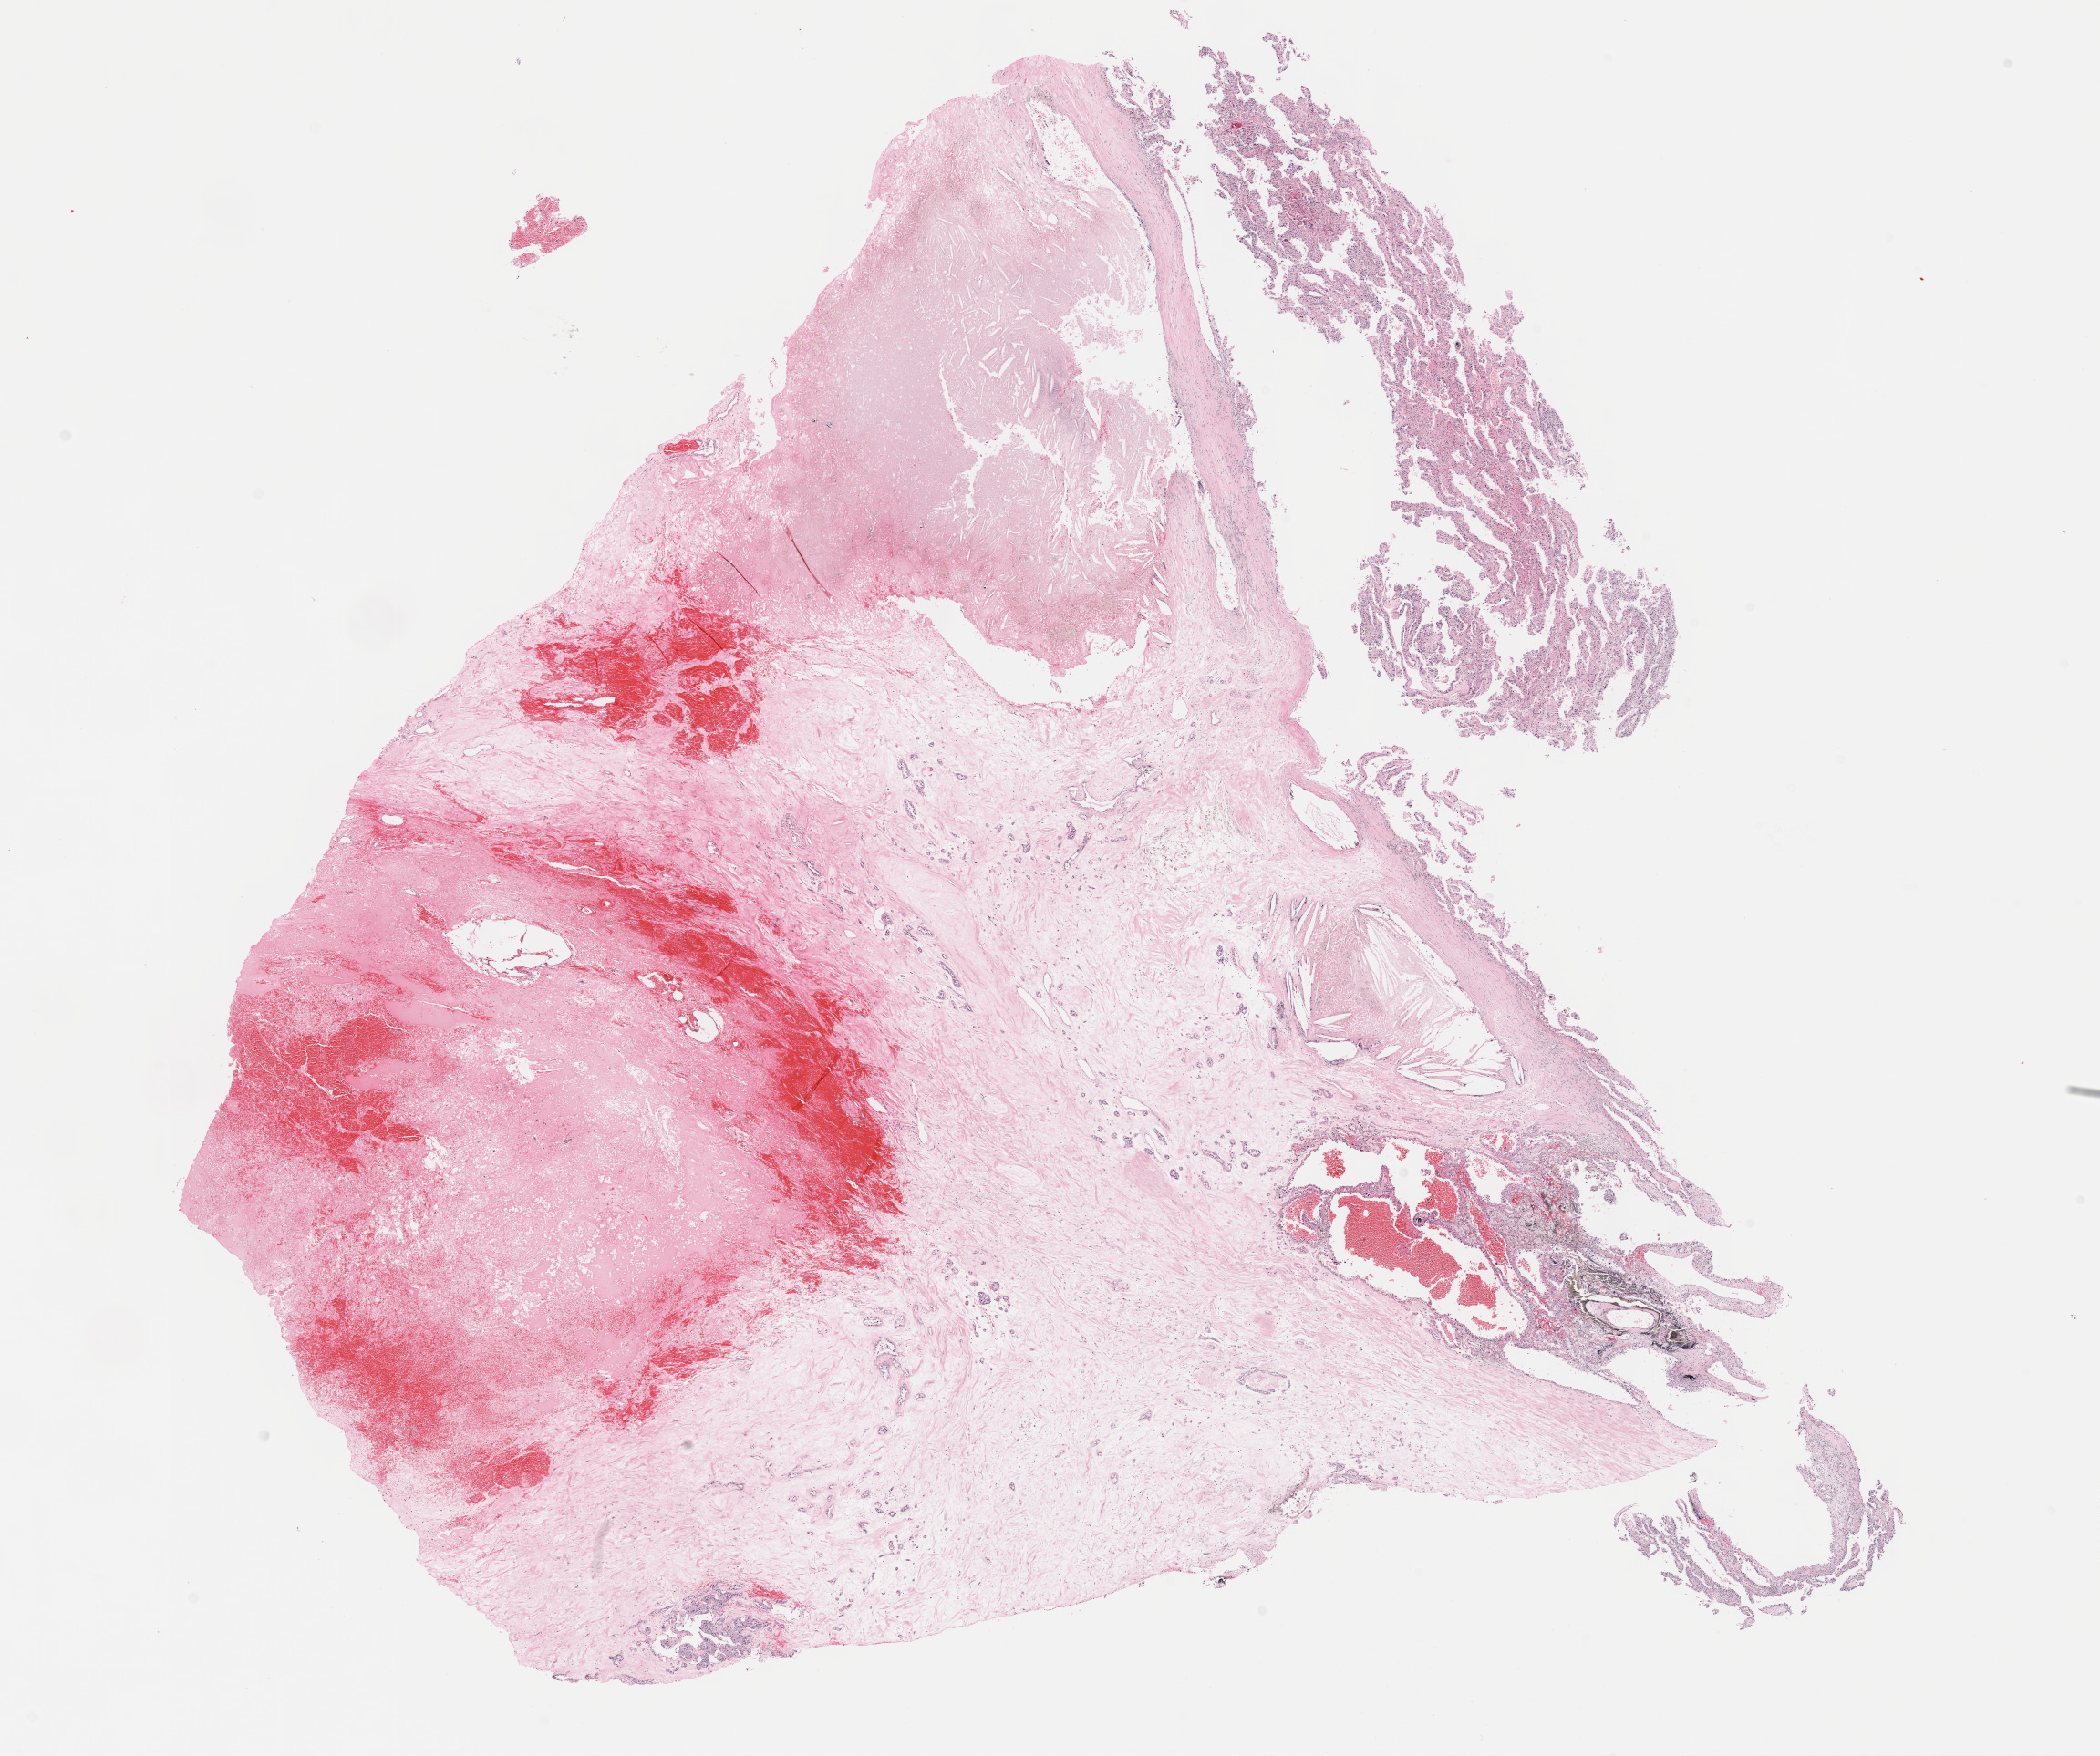
Whole-slide histology image, Hematoxylin and eosin (H&E) stained — low-resolution overview of the scanned area, about 18.6 x 15.6 mm (slide scanned at 40x); formalin-fixed paraffin-embedded (FFPE) diagnostic section; sample: primary tumour, kidney. Male patient; age at initial diagnosis 48 years. Histologic grade: G3 (poorly differentiated).
TNM: T2 N0 M0. Diagnosis: Clear cell adenocarcinoma, NOS. AJCC pathologic stage: II. Laterality: right.